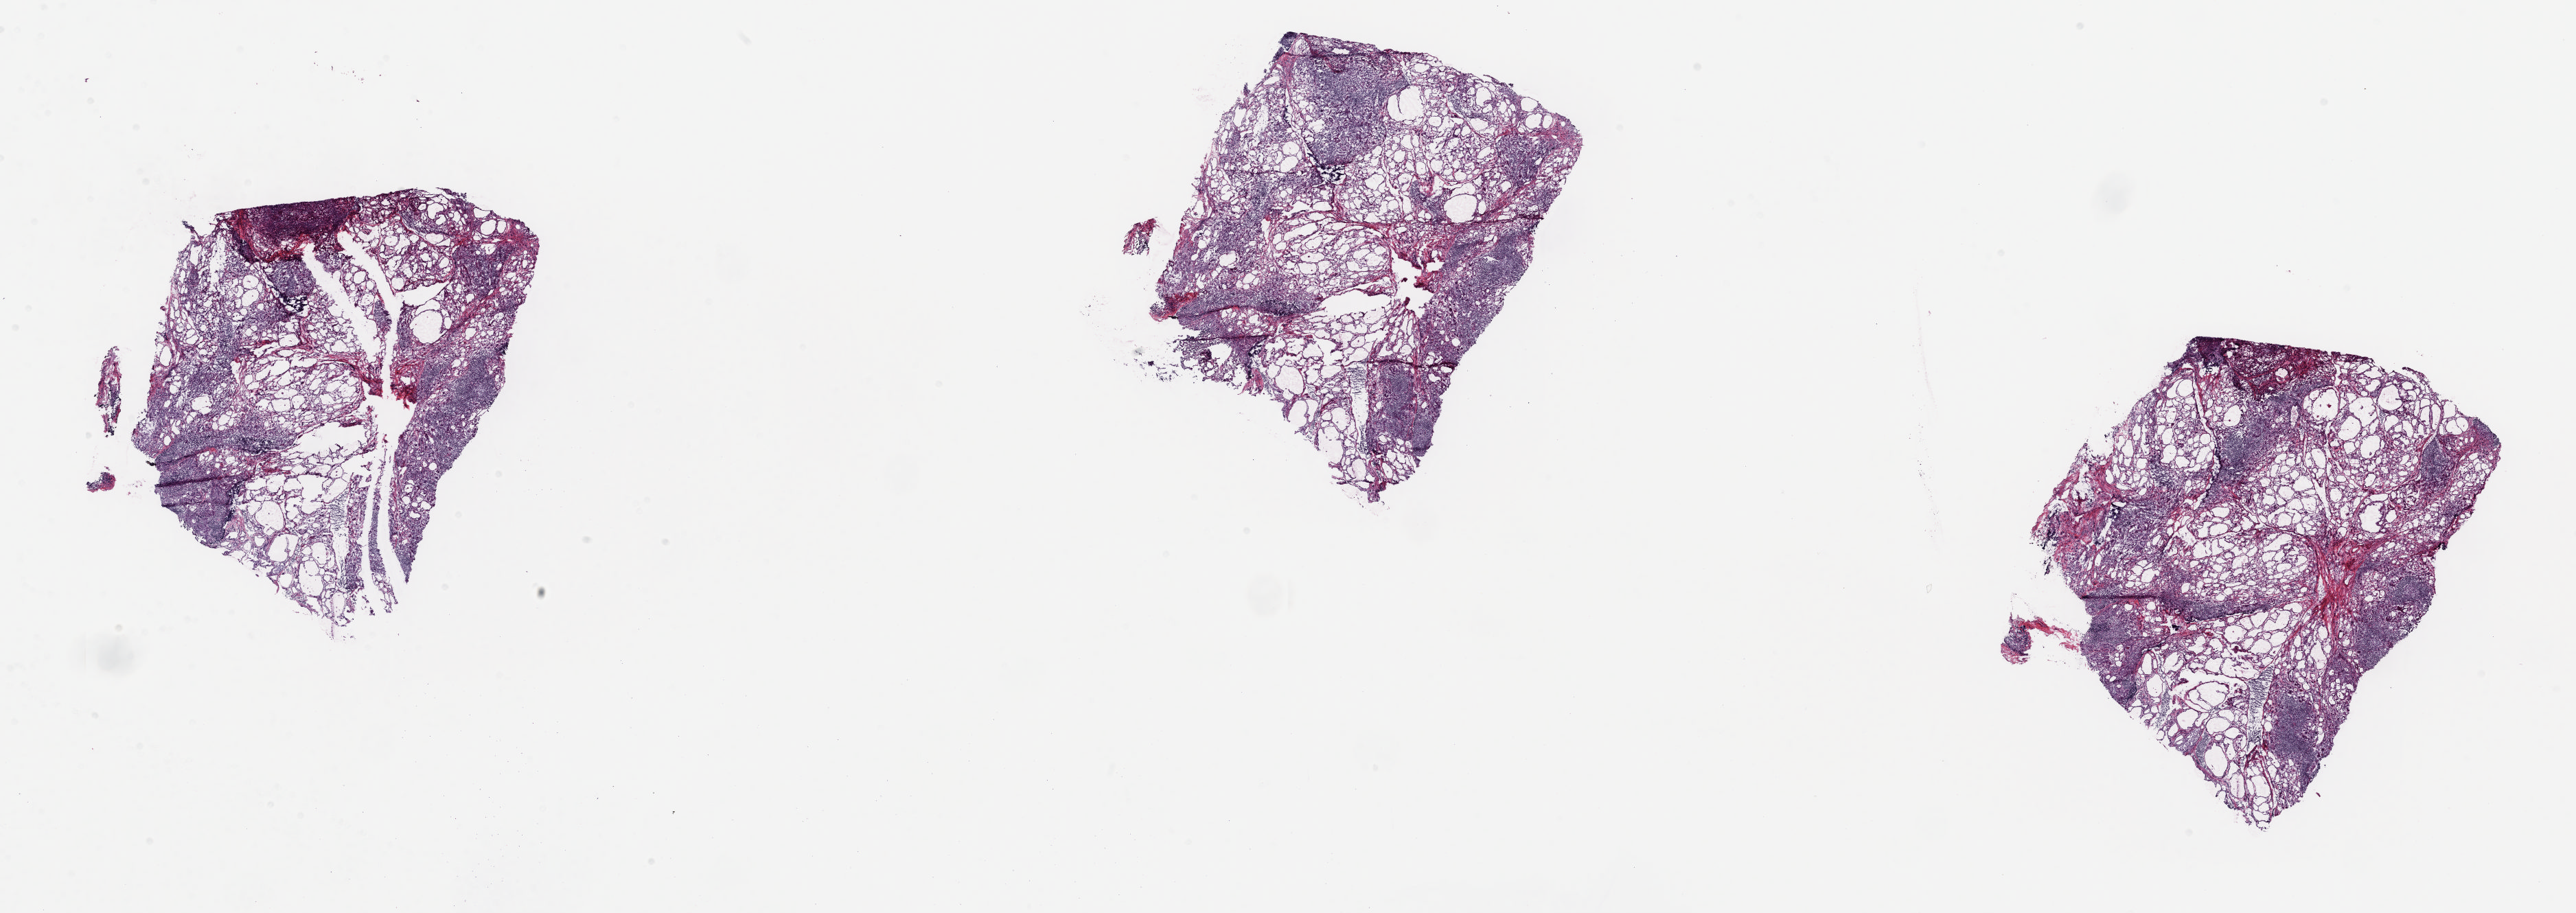
Whole-slide histology image, Hematoxylin and eosin (H&E) stained — whole scanned area (about 29.8 x 10.5 mm) shown as a low-resolution overview. Frozen section from the top of the tissue portion. Solid tissue normal (non-tumour tissue) sample from the thyroid. Female, age 32 years at initial diagnosis. Pathologist review of this section (percent, as recorded): tumour cells 0%, tumour nuclei 0%, normal cells 100%, stromal cells 0%, necrosis 0%. Infiltration values recorded for this section: lymphocyte infiltration 0%, monocyte infiltration 0%, neutrophil infiltration 0%.
This section: solid tissue normal sample (biorepository sample class). Patient diagnosis: Papillary carcinoma, columnar cell (thyroid gland).